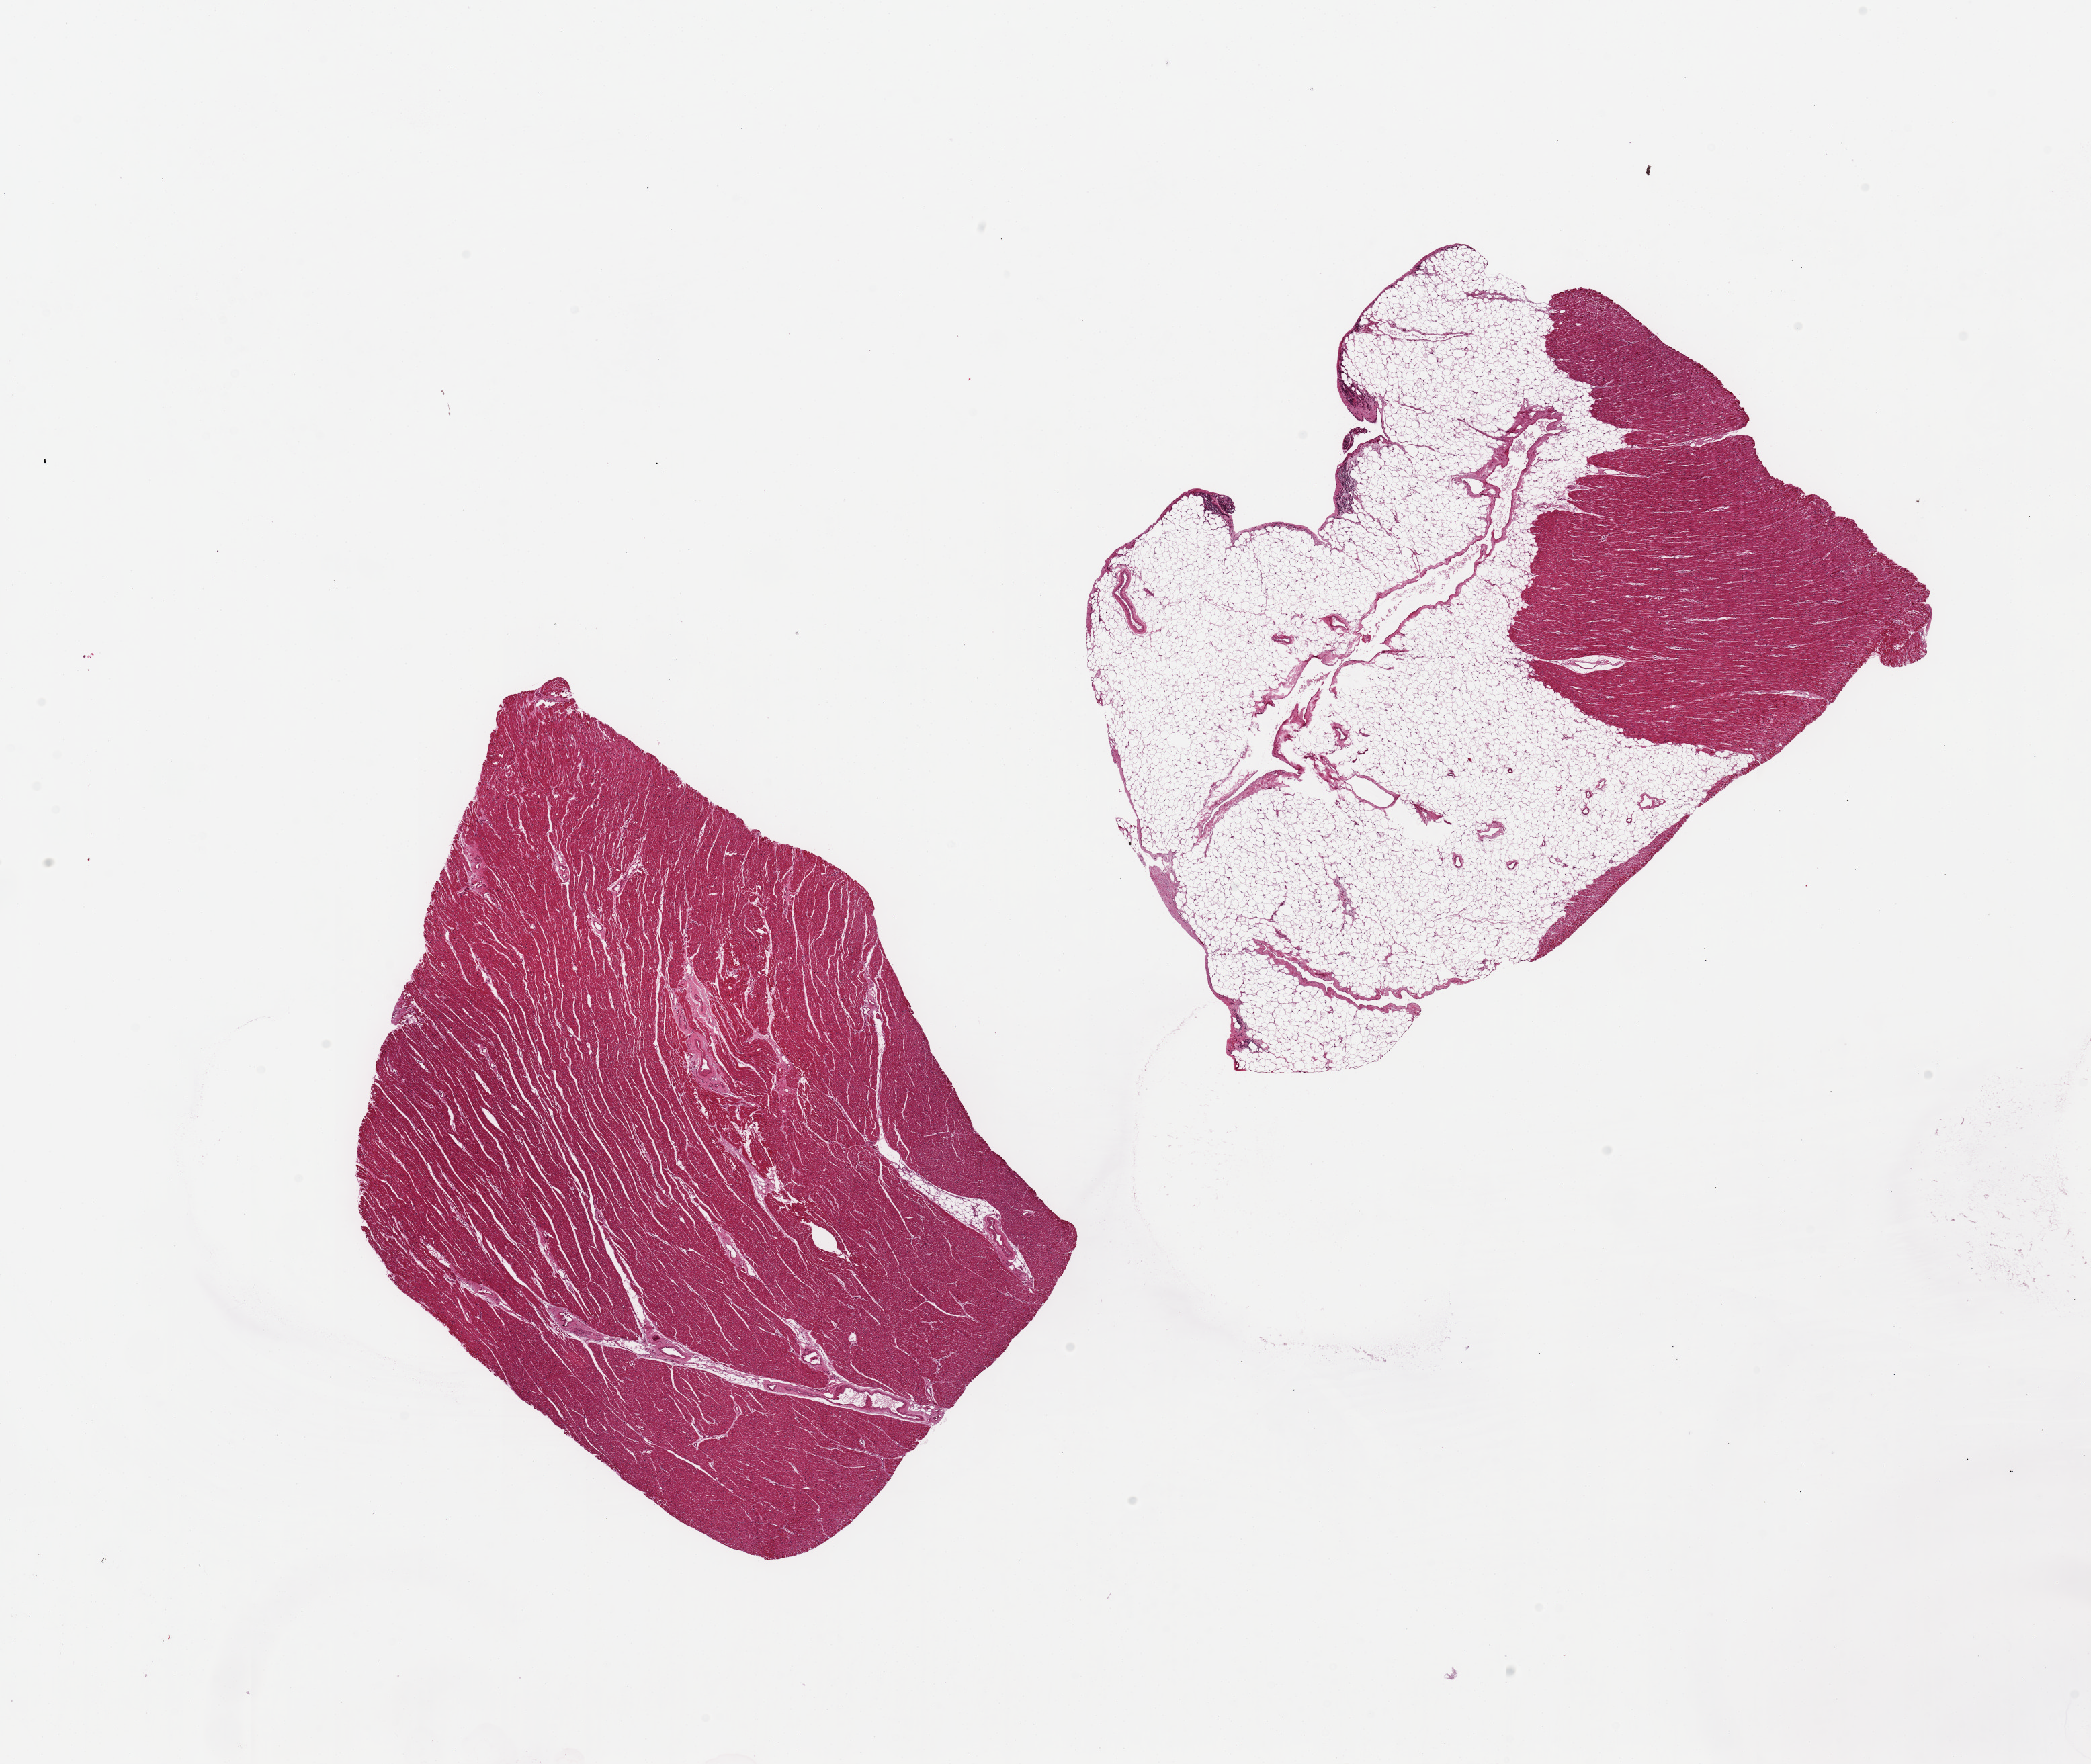
Whole-slide image, H&E stain, a low-resolution overview of the entire scanned area, about 24.6 x 20.8 mm (acquisition: 20x scan), PAXgene-fixed paraffin-embedded (PFPE) section, sampled site (target tissue): heart, tissue donor sample. Donor: female.
• pathologist's review note for this sample: 2 pieces, 9x7 & 10x8mm; 1 is 70% adipose; other is all myocardium